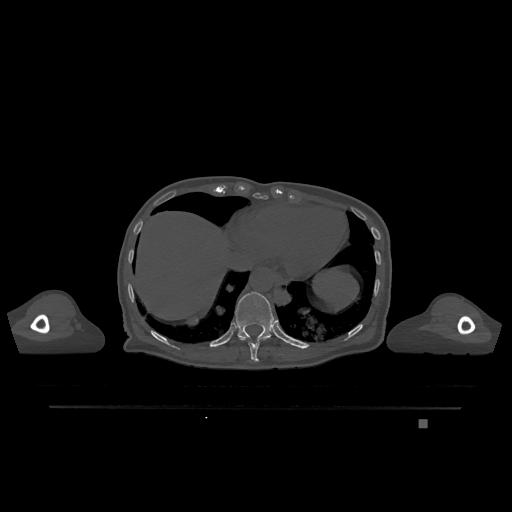
CT including the spine, one axial slice; bone window (W 1800 / L 400 HU); 512 × 512 image matrix, field of view 500 × 500 mm. Female patient, age 74 years. Case-level facts recorded for this patient, not image findings: primary cancer: lung.
Annotated regions visible in this slice (semi-automatically segmented with operator editing):
- T10 vertebra: bounding box (x1, y1, x2, y2) in pixels: (239, 337, 268, 362)
- T11 vertebra: (228, 291, 275, 341)